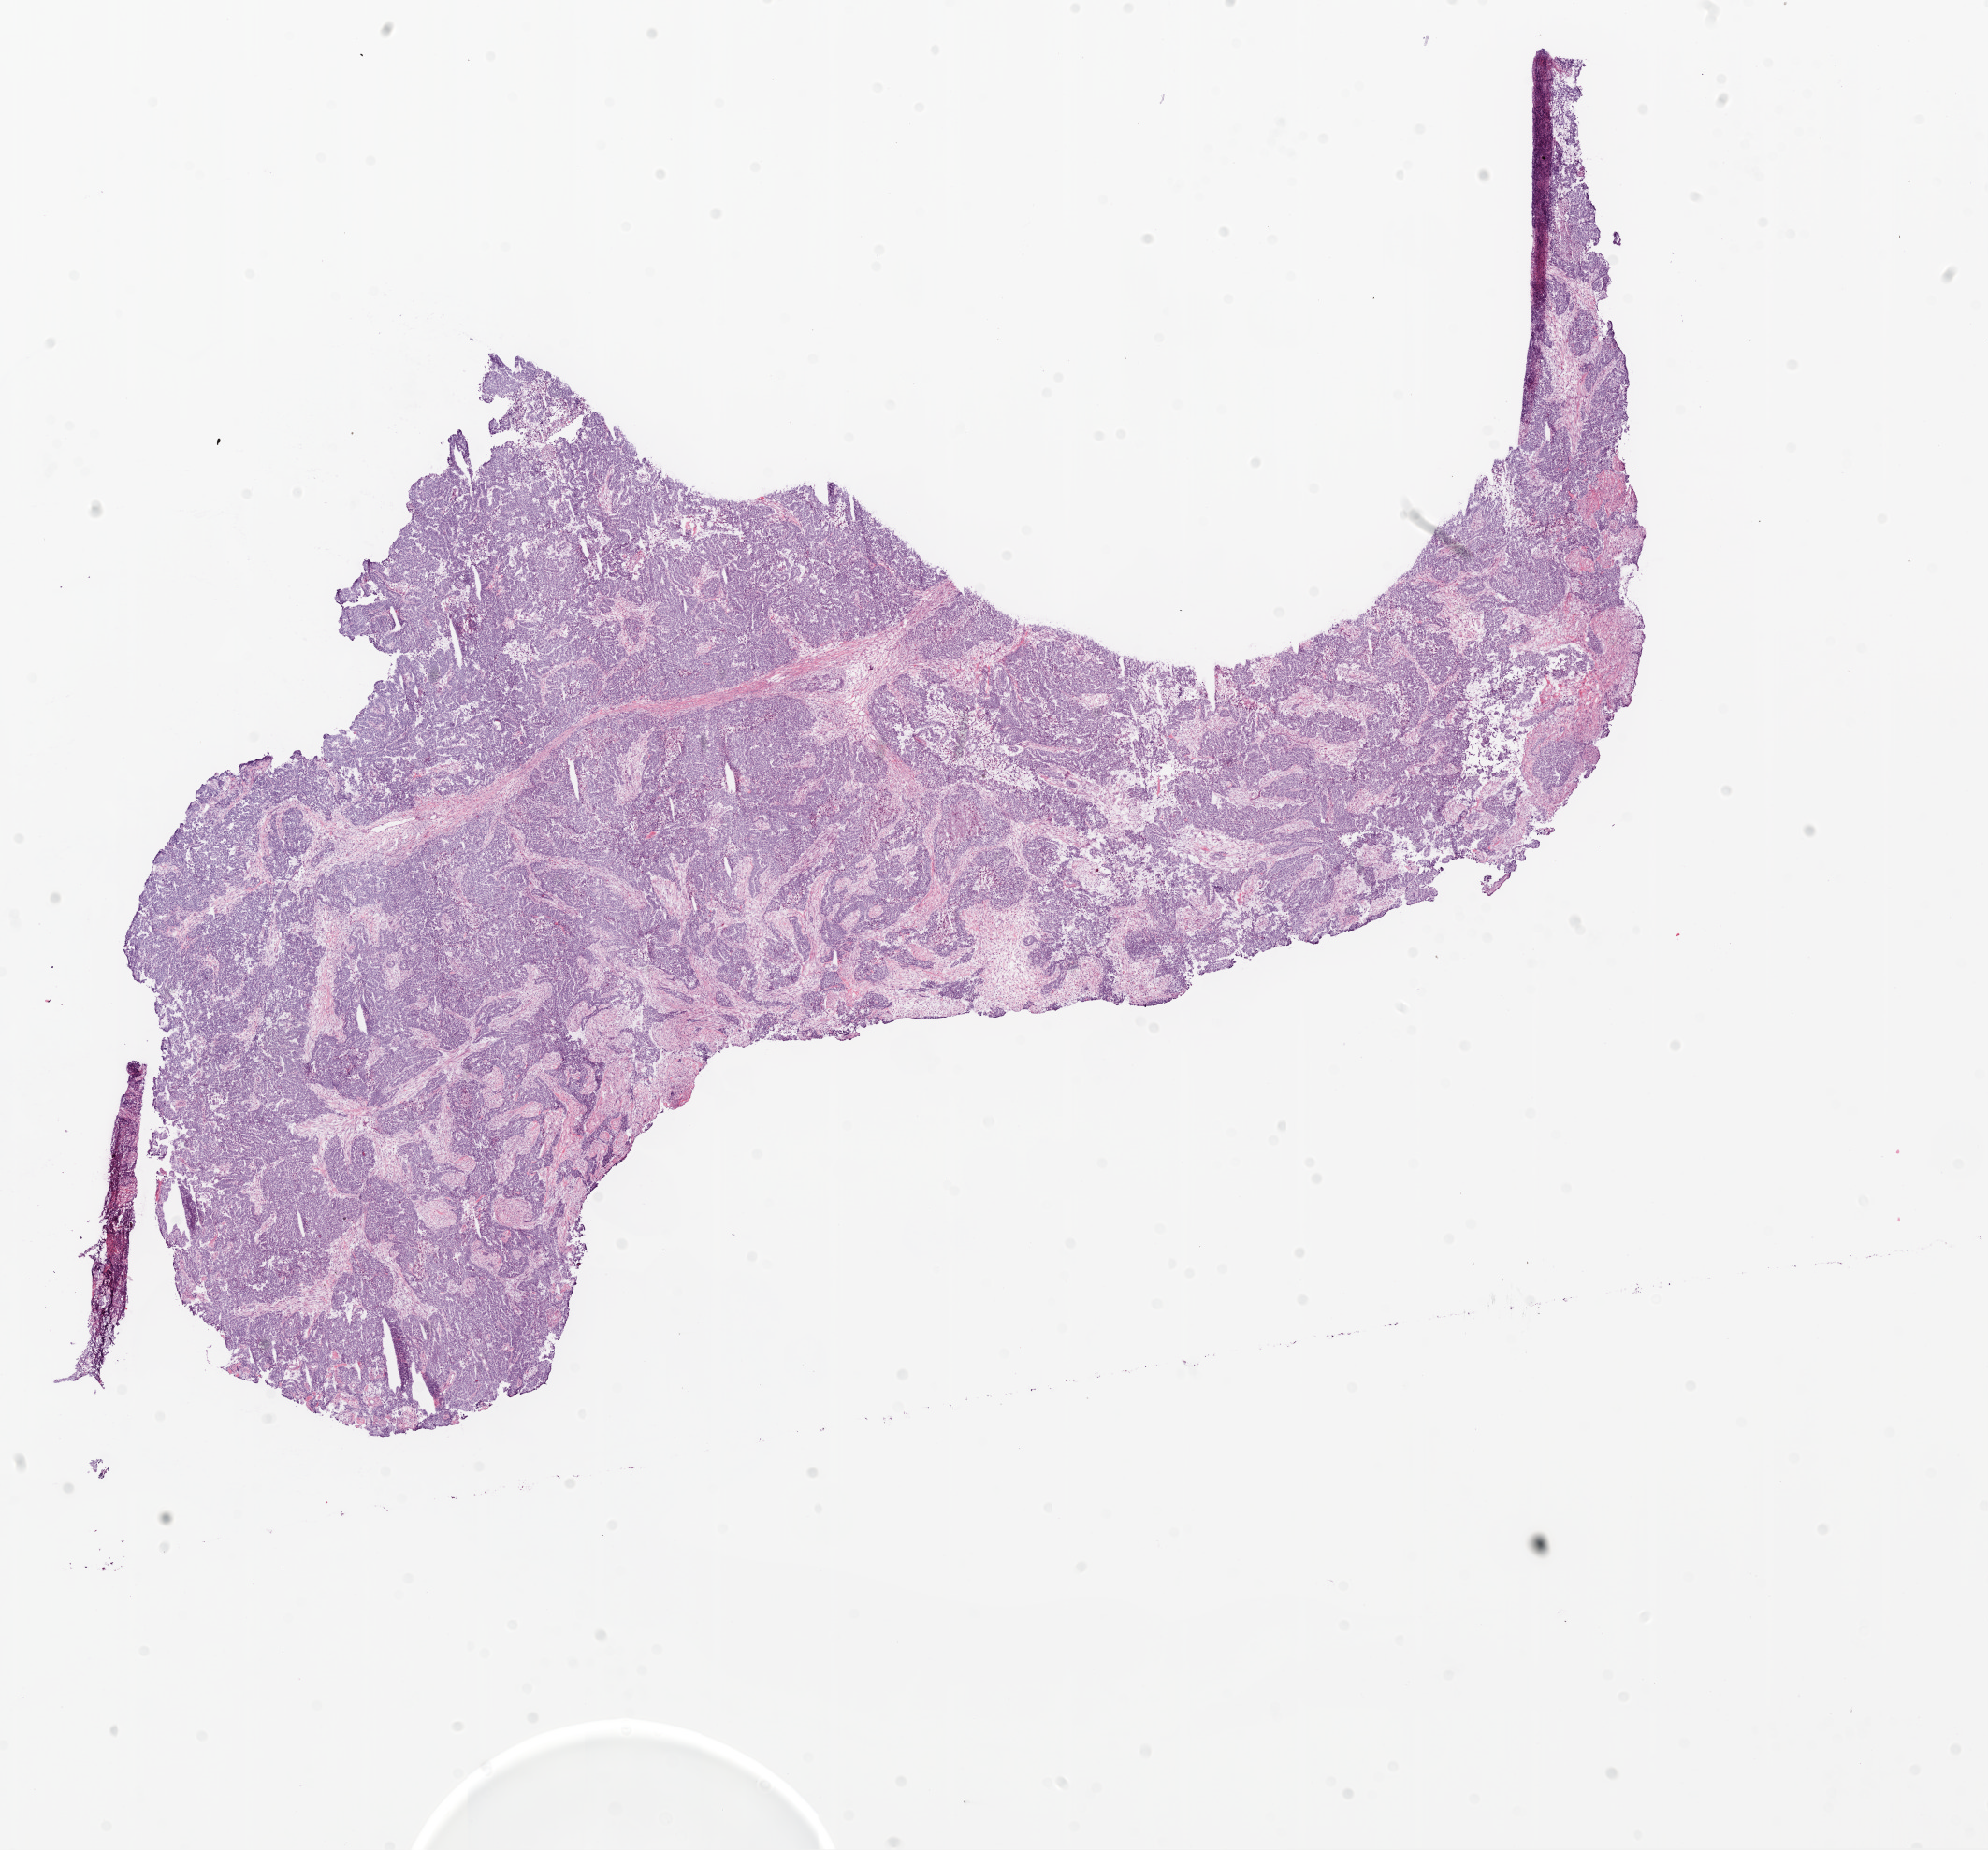
Digitized Hematoxylin and eosin (H&E) stained tissue section (whole slide) — whole scanned area (about 17.1 x 15.9 mm) shown as a low-resolution overview; frozen section from the bottom of the tissue portion; primary tumour sample from the ovary. Patient: female, age at initial diagnosis 80 years. Histologic grade: G3 (poorly differentiated). Composition of this section per pathologist review: tumour cells 80%, tumour nuclei 85%, normal cells 1%, stromal cells 14%, necrosis 5%.
Histologic diagnosis: Serous cystadenocarcinoma, NOS. FIGO stage: IIIC.